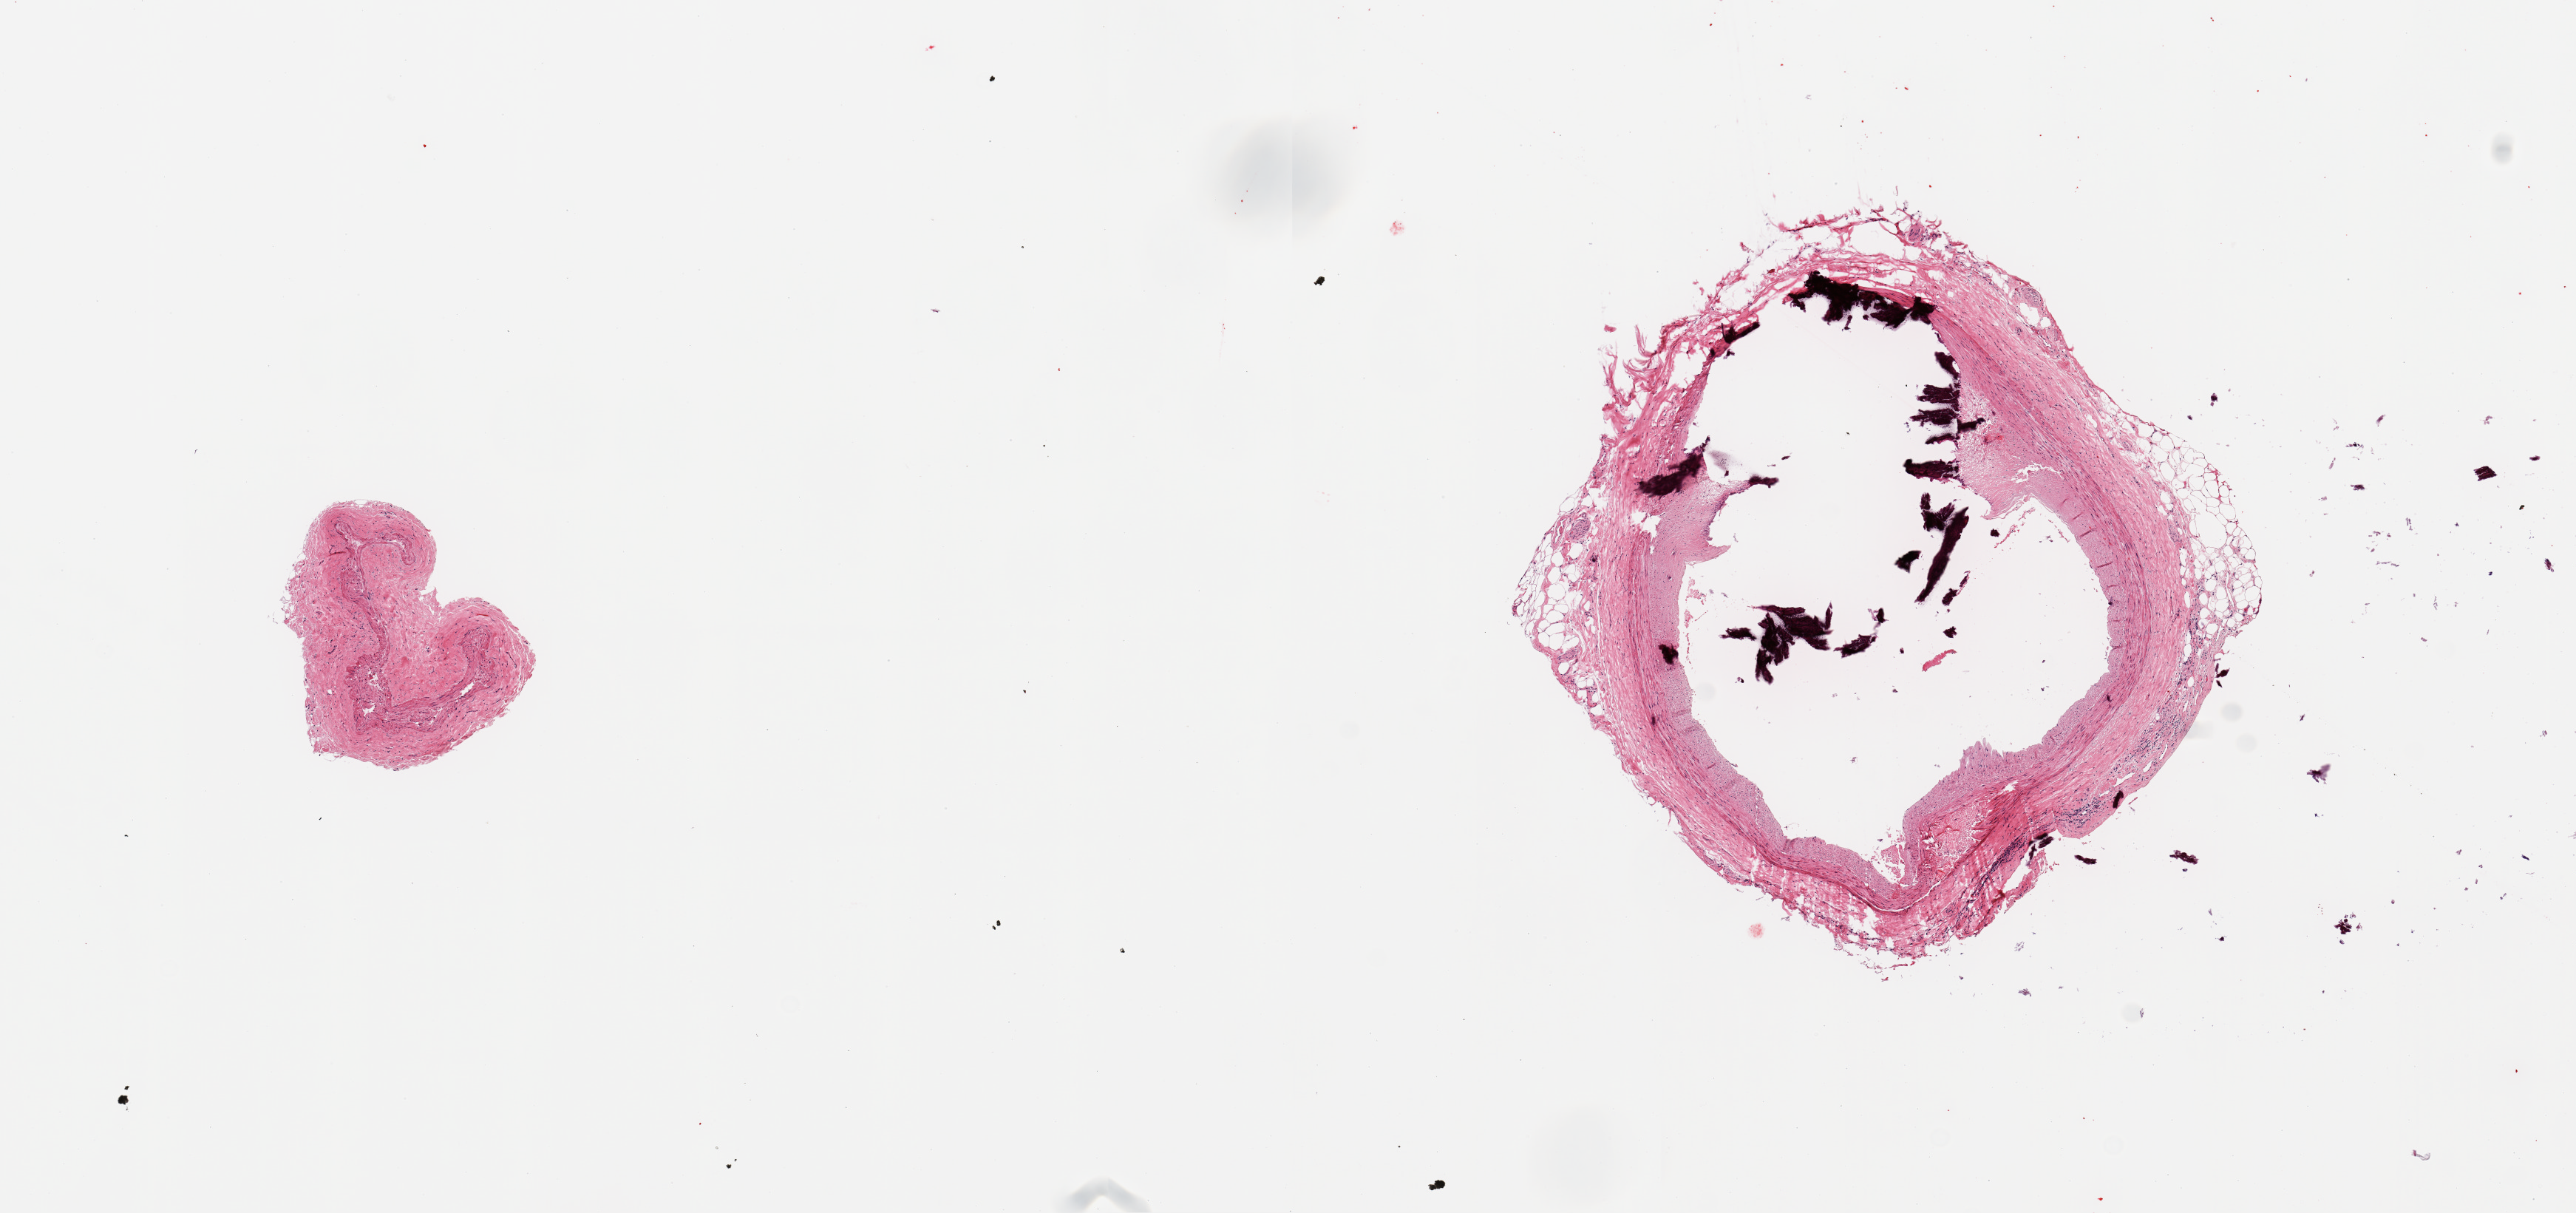
Digitized hematoxylin and eosin (H&E)-stained section — a low-resolution overview of the entire scanned area, about 13.8 x 6.5 mm (from a 20x scan); PAXgene-fixed, paraffin-embedded tissue; target tissue: coronary artery; tissue donor sample. Female donor.
- pathologist's review note for this sample: 2 pieces: larger has severe calcified mural sclerosis; smaller is a vein